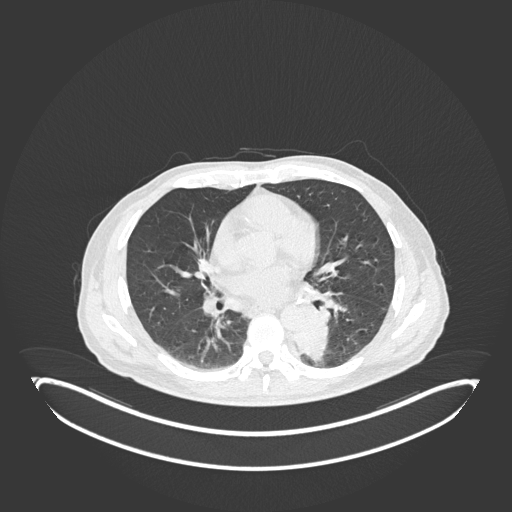
Chest CT, one axial slice; position 93 of 251 along the scan axis; reconstruction kernel B30f; 120 kVp; lung window (W 1500 / L -600 HU); 1 mm slice thickness; 512 × 512 image matrix, field of view 500 × 500 mm. Male patient, age 72 years. Case-level facts recorded for this patient, not image findings: clinical TNM (as recorded): T2b N0 M1.
Outlined on this slice (rectangle marked by the reading radiologist):
- lung tumour (recorded histology: adenocarcinoma): bounding box (x1, y1, x2, y2) in pixels: (293, 321, 335, 368)